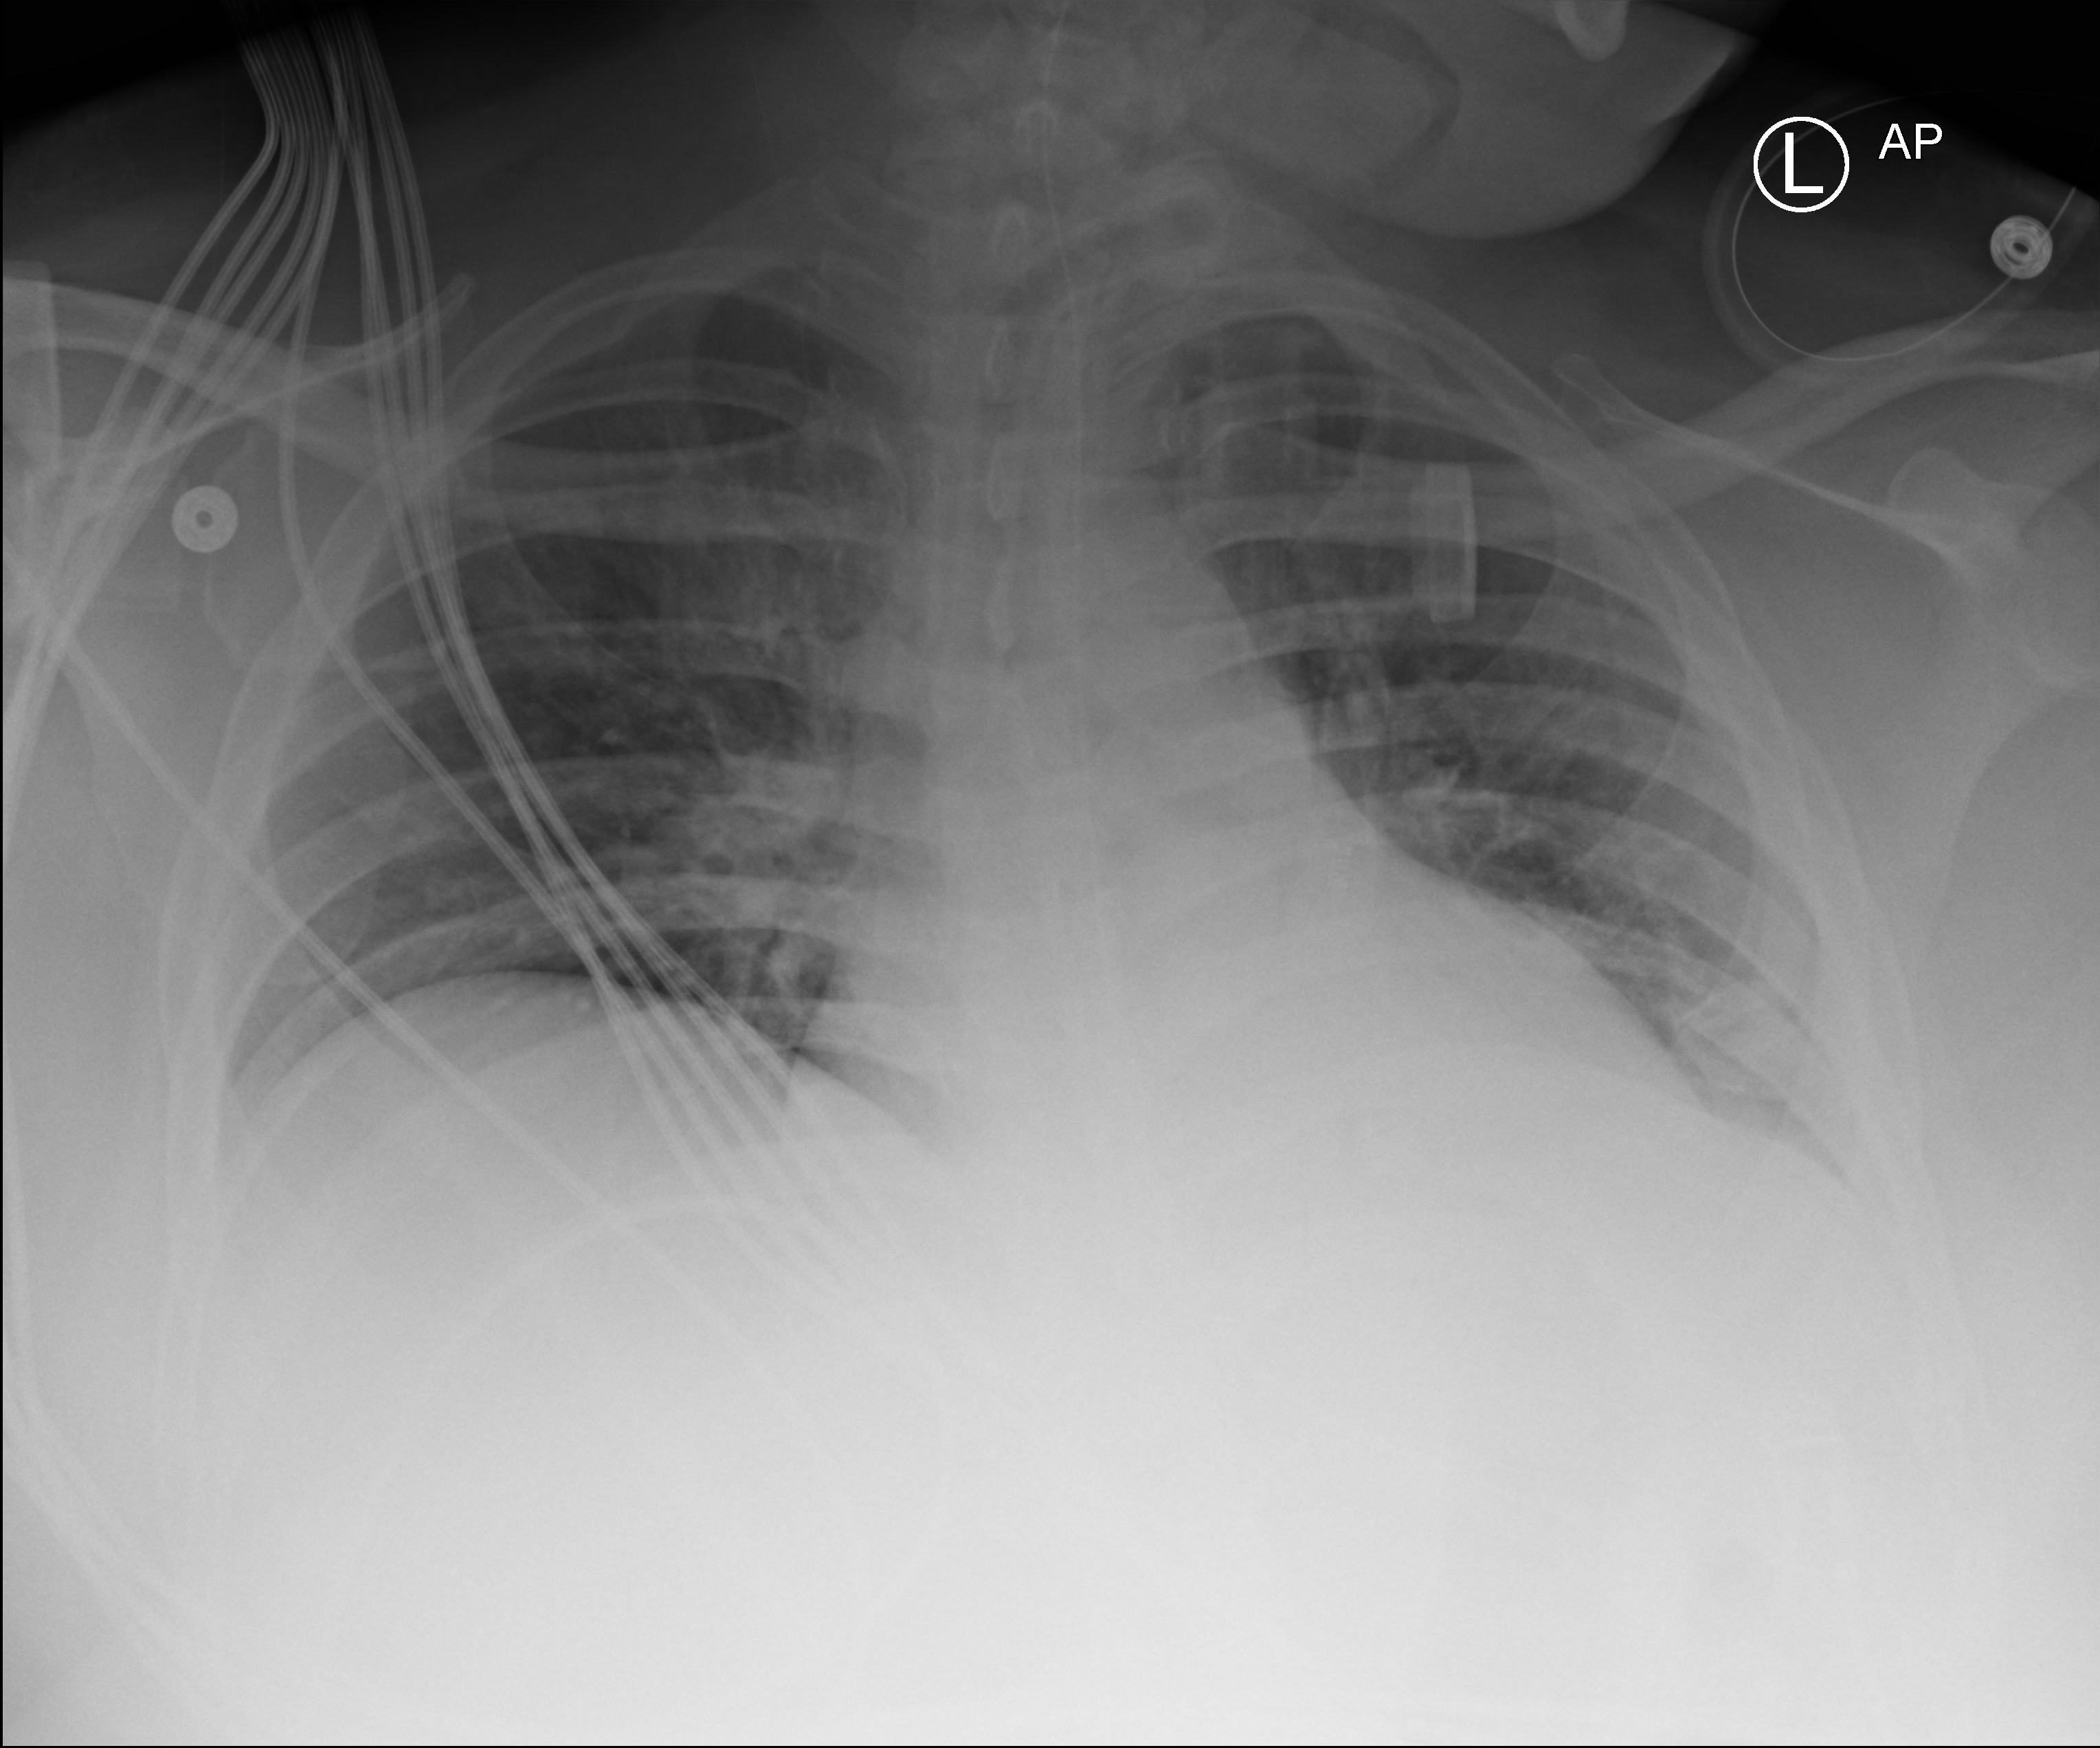
Chest X-ray (portable), anteroposterior (AP) projection. Male patient hospitalised with COVID-19, age 18–59 years.
From the hospital-stay record, not from the radiograph (when in the stay this image was taken is not recorded):
- other chronic lung disease (admission record): yes
- admitted to intensive care during this hospital stay: yes